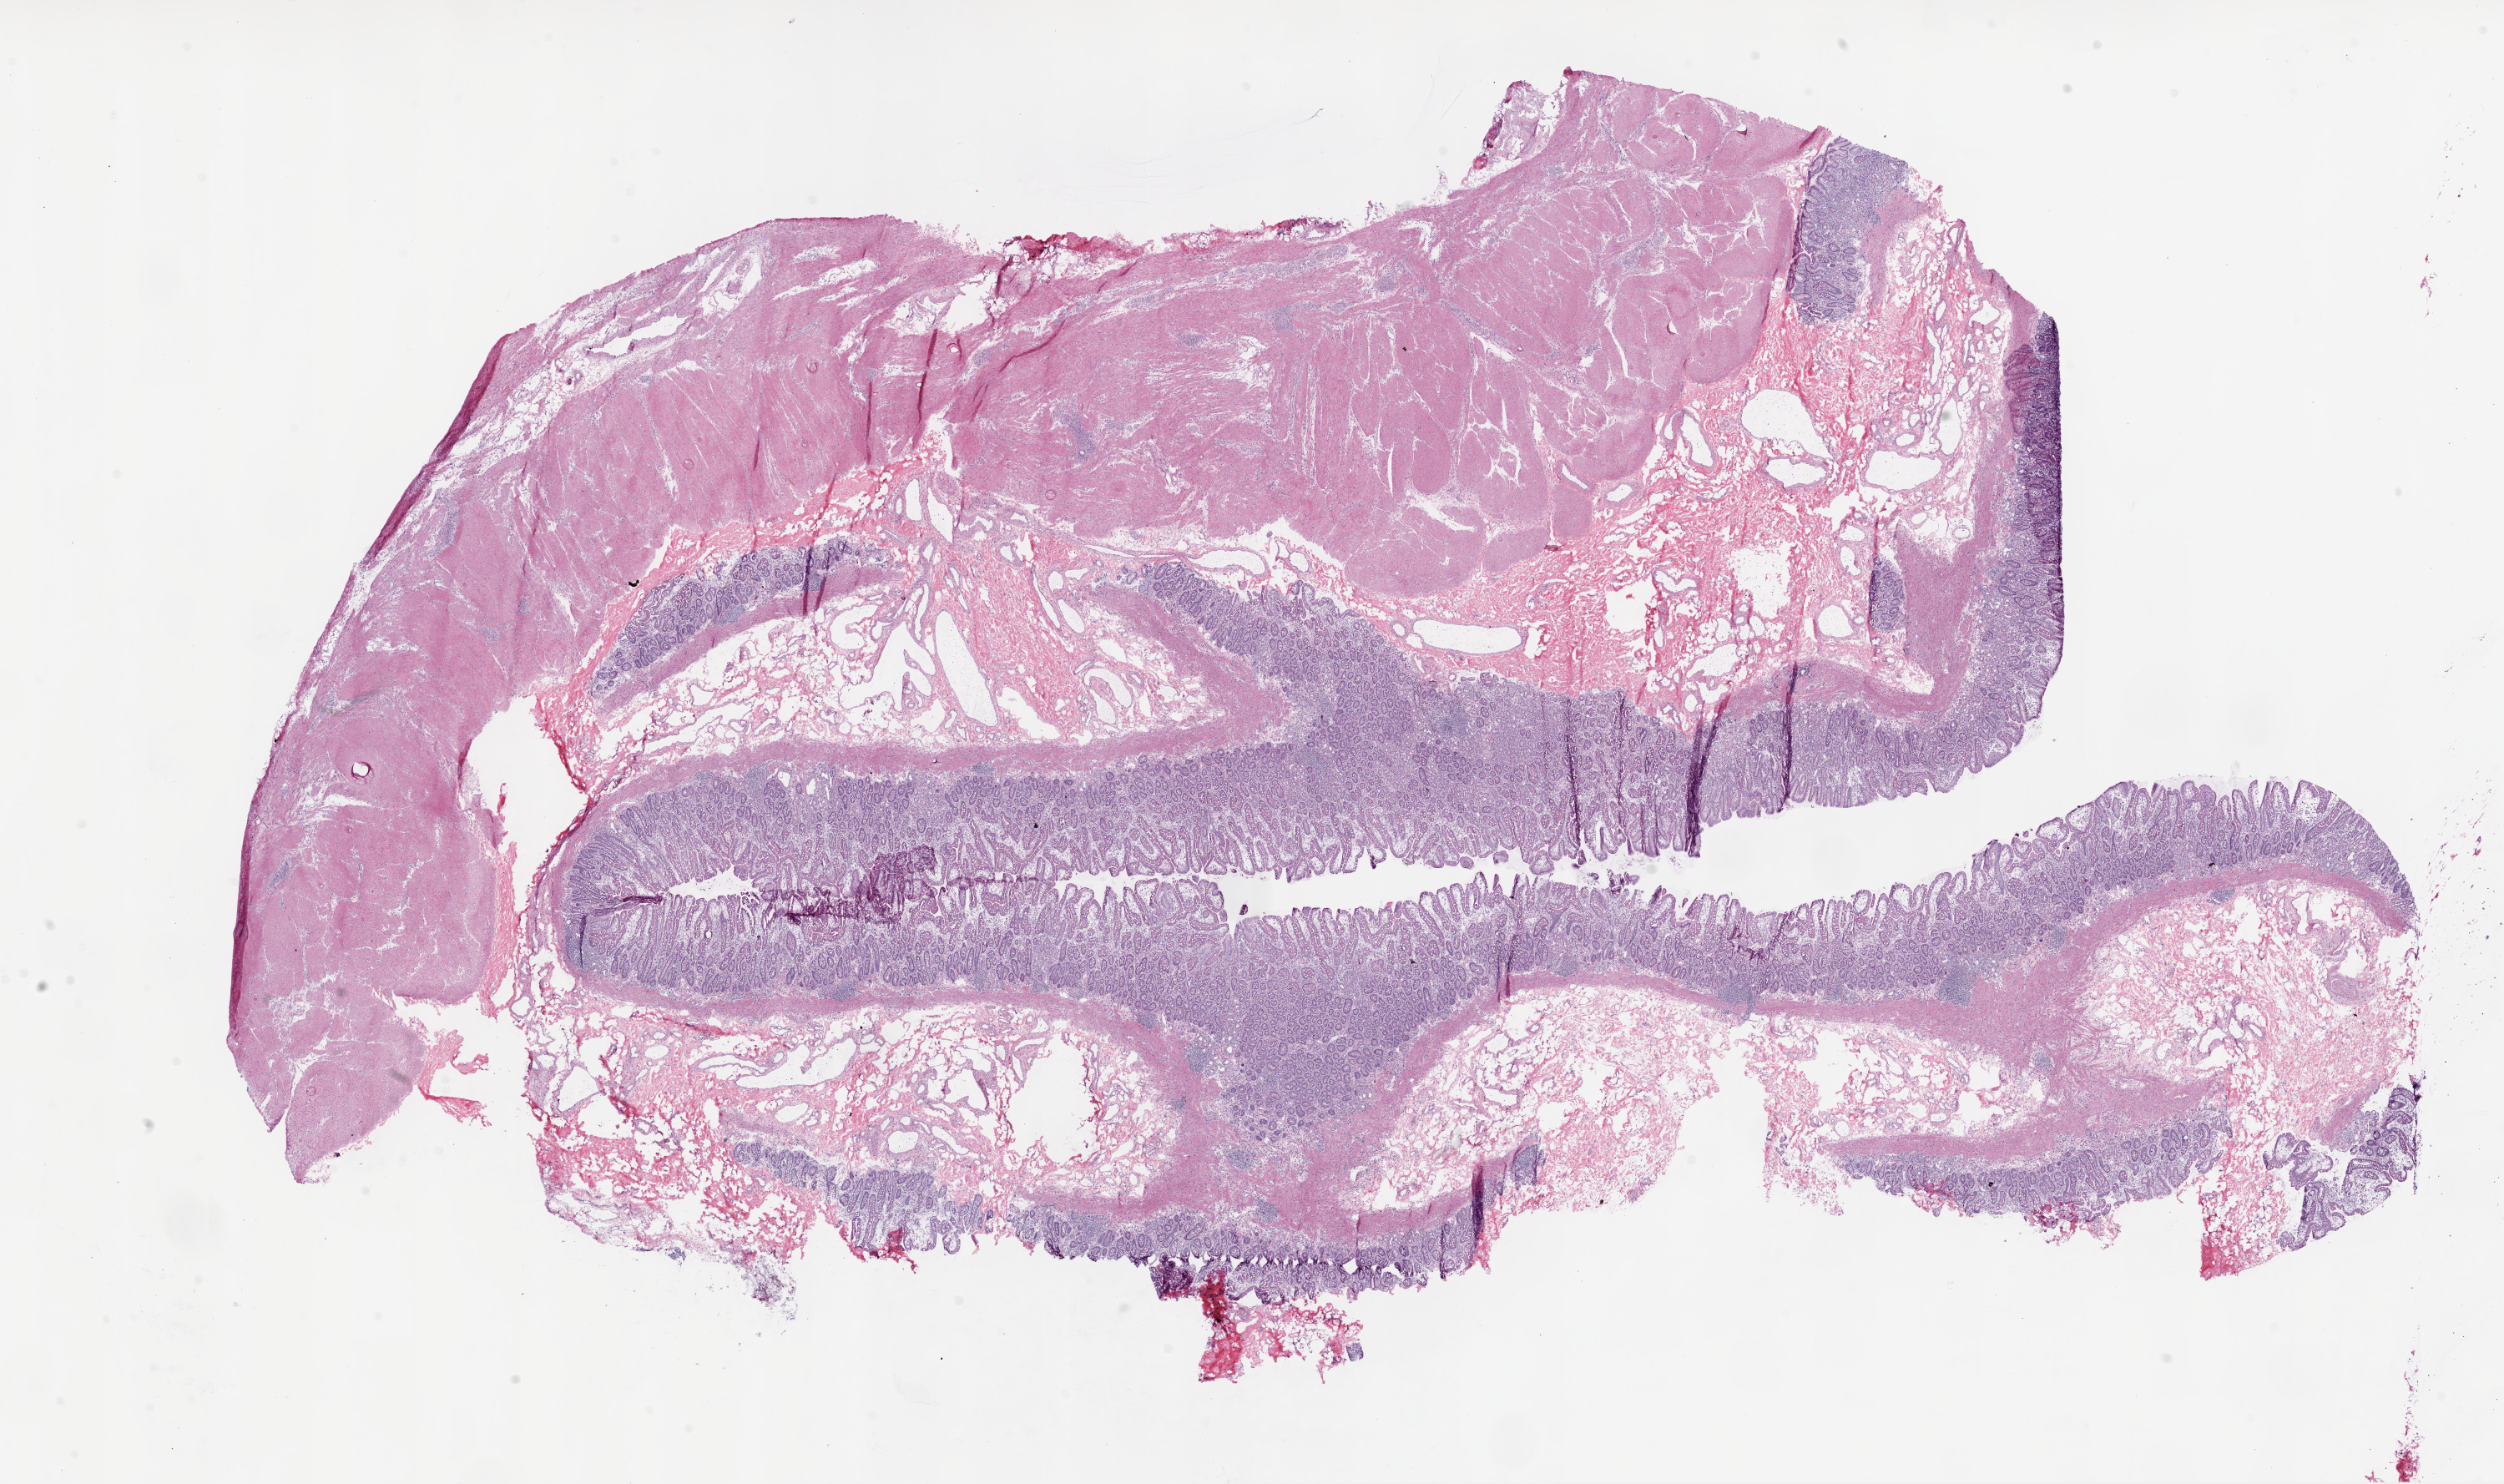
Digitized H&E tissue section (whole slide) — low-resolution overview of the scanned area, about 24.1 x 14.3 mm (slide scanned at 20x). Frozen section from the bottom of the tissue portion. Sample: solid tissue normal (non-tumour tissue), stomach. Patient: male, age at initial diagnosis 75 years.
- this section: solid tissue normal (non-tumour) sample from the same patient
- patient diagnosis: Adenocarcinoma, NOS (cardia, NOS)